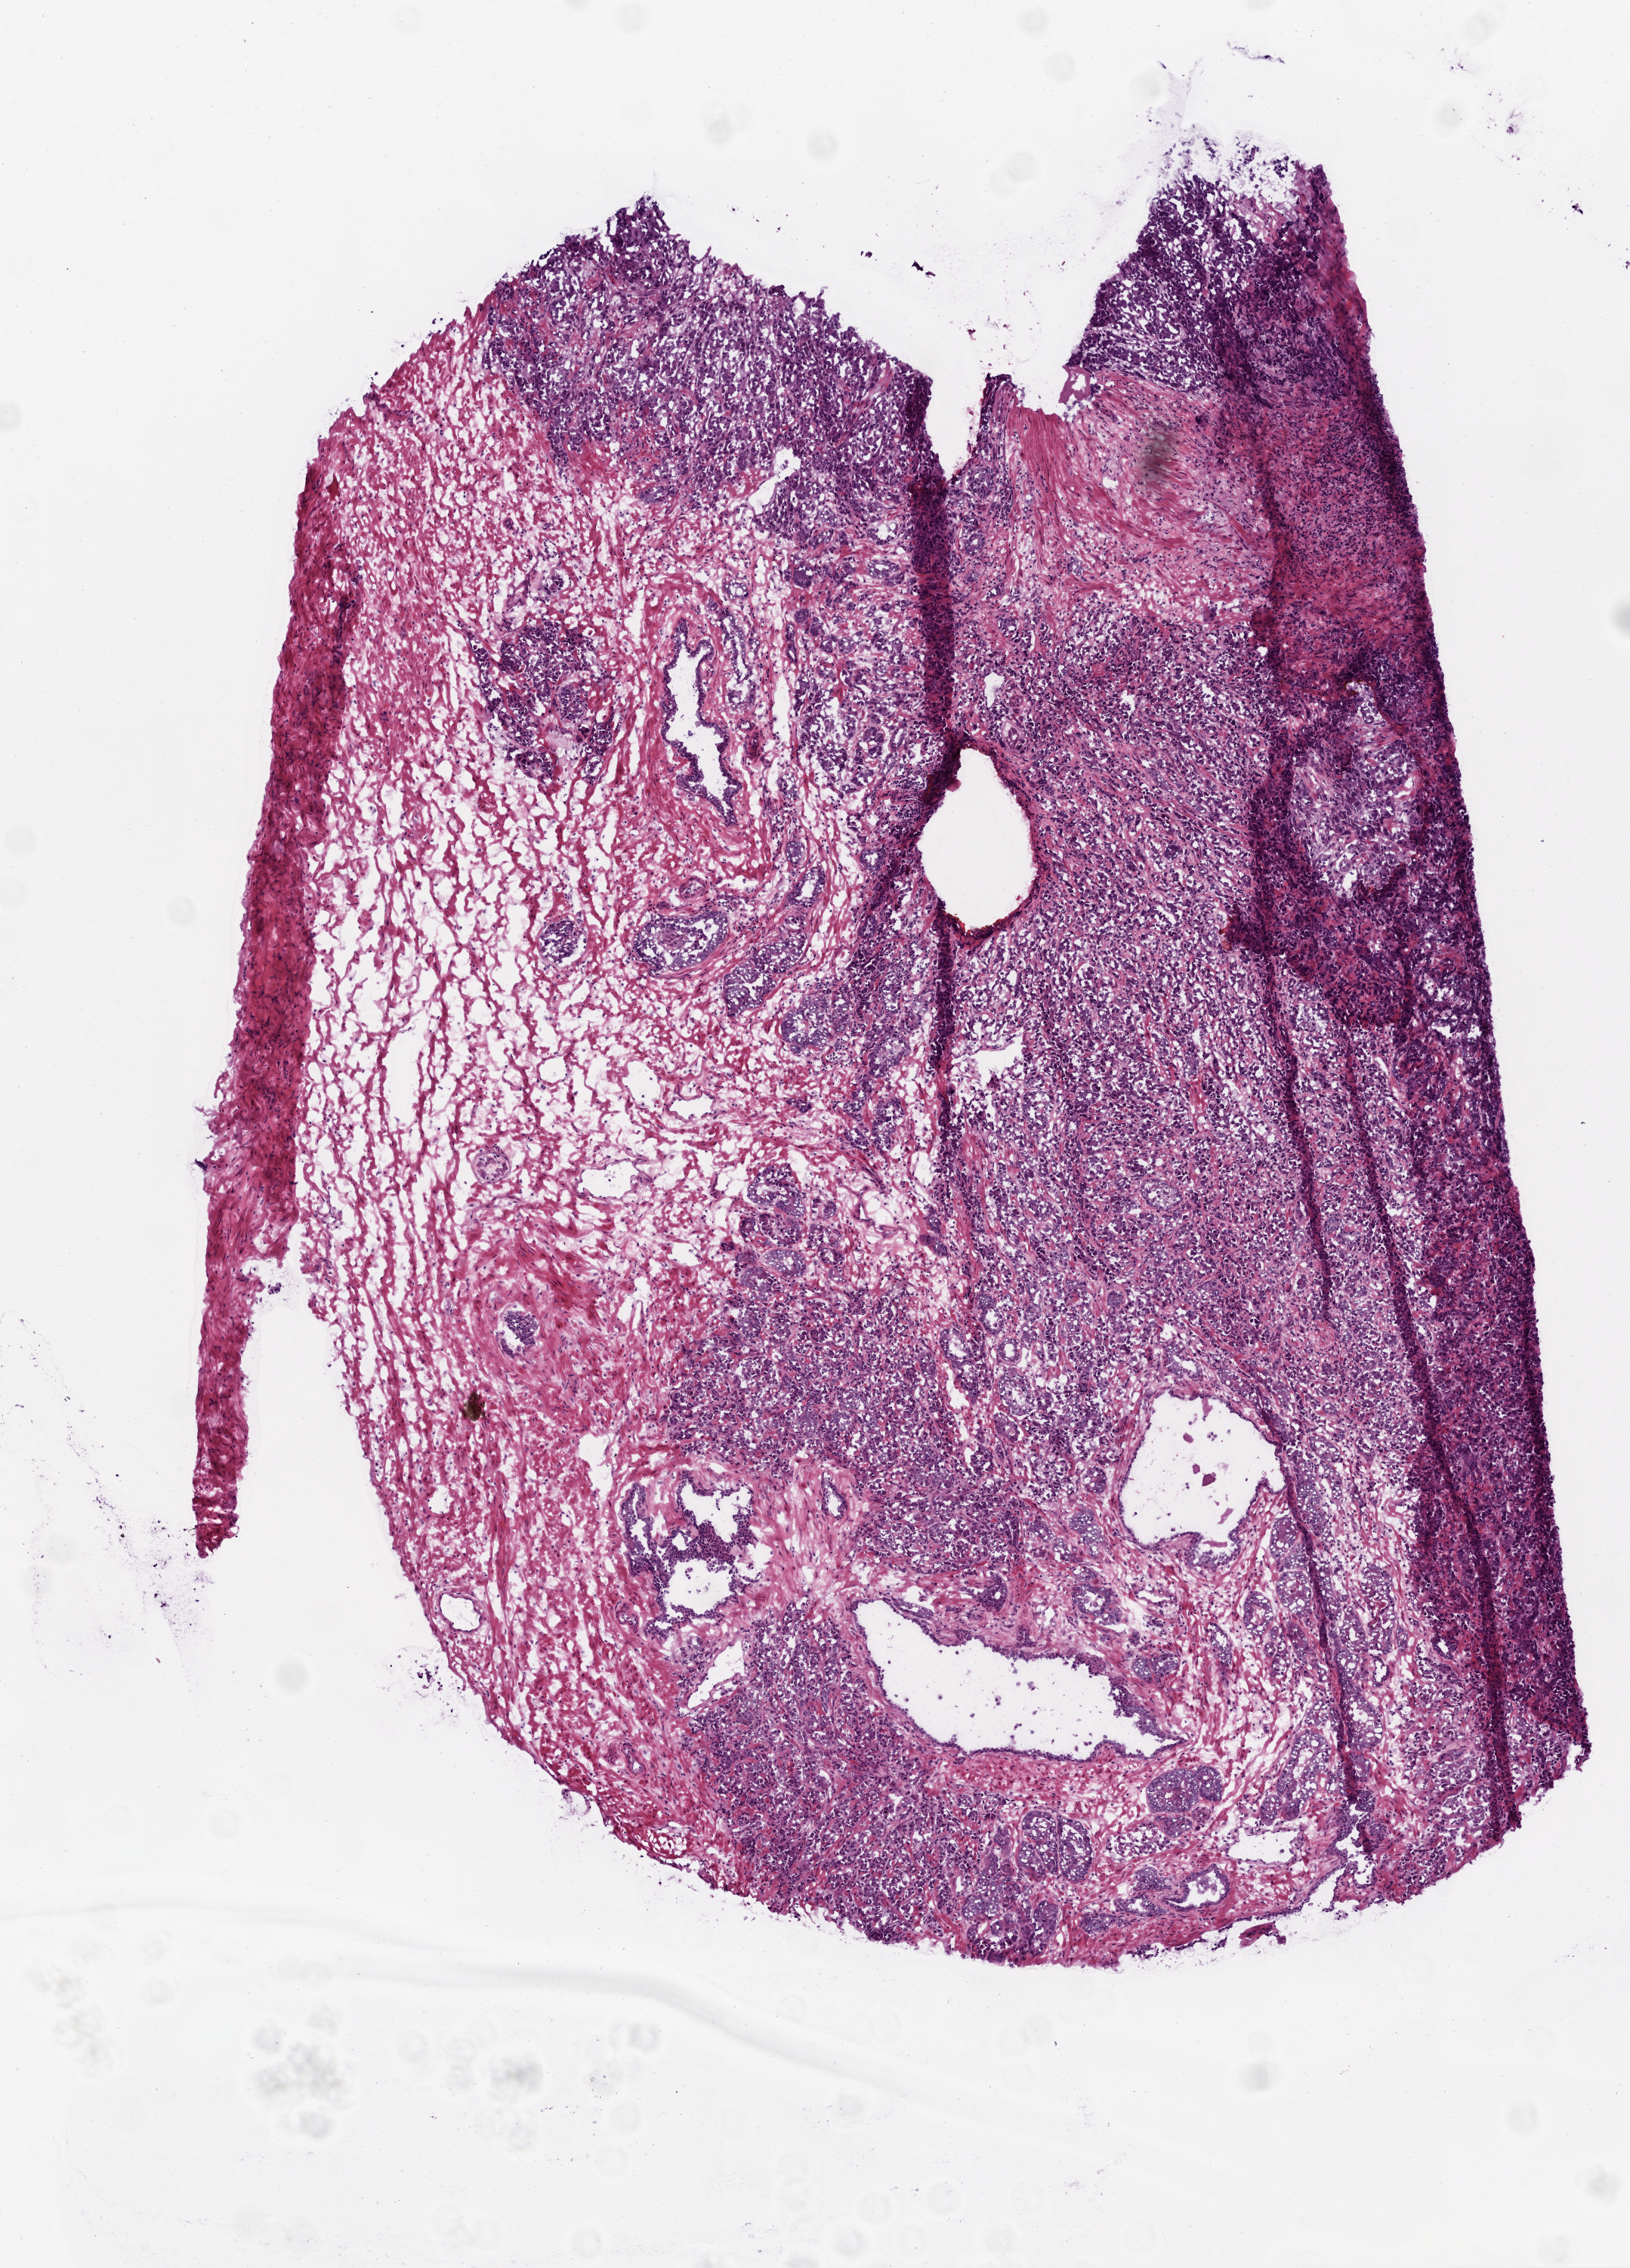
Hematoxylin and eosin (H&E) stained whole-slide image, shown as a low-resolution overview of the whole scanned area (about 4.4 x 6.1 mm), frozen section from the top of the tissue portion, prostate, primary tumour sample. Male, age 58 years at initial diagnosis. Gleason score: 7 (4+3). Composition of this section per pathologist review: tumour cells 85%, tumour nuclei 85%, normal cells 5%, stromal cells 10%, necrosis 0%.
Diagnosis: Acinar cell carcinoma (prostate gland). Lymph nodes positive (case pathology): 0 of 3 examined.